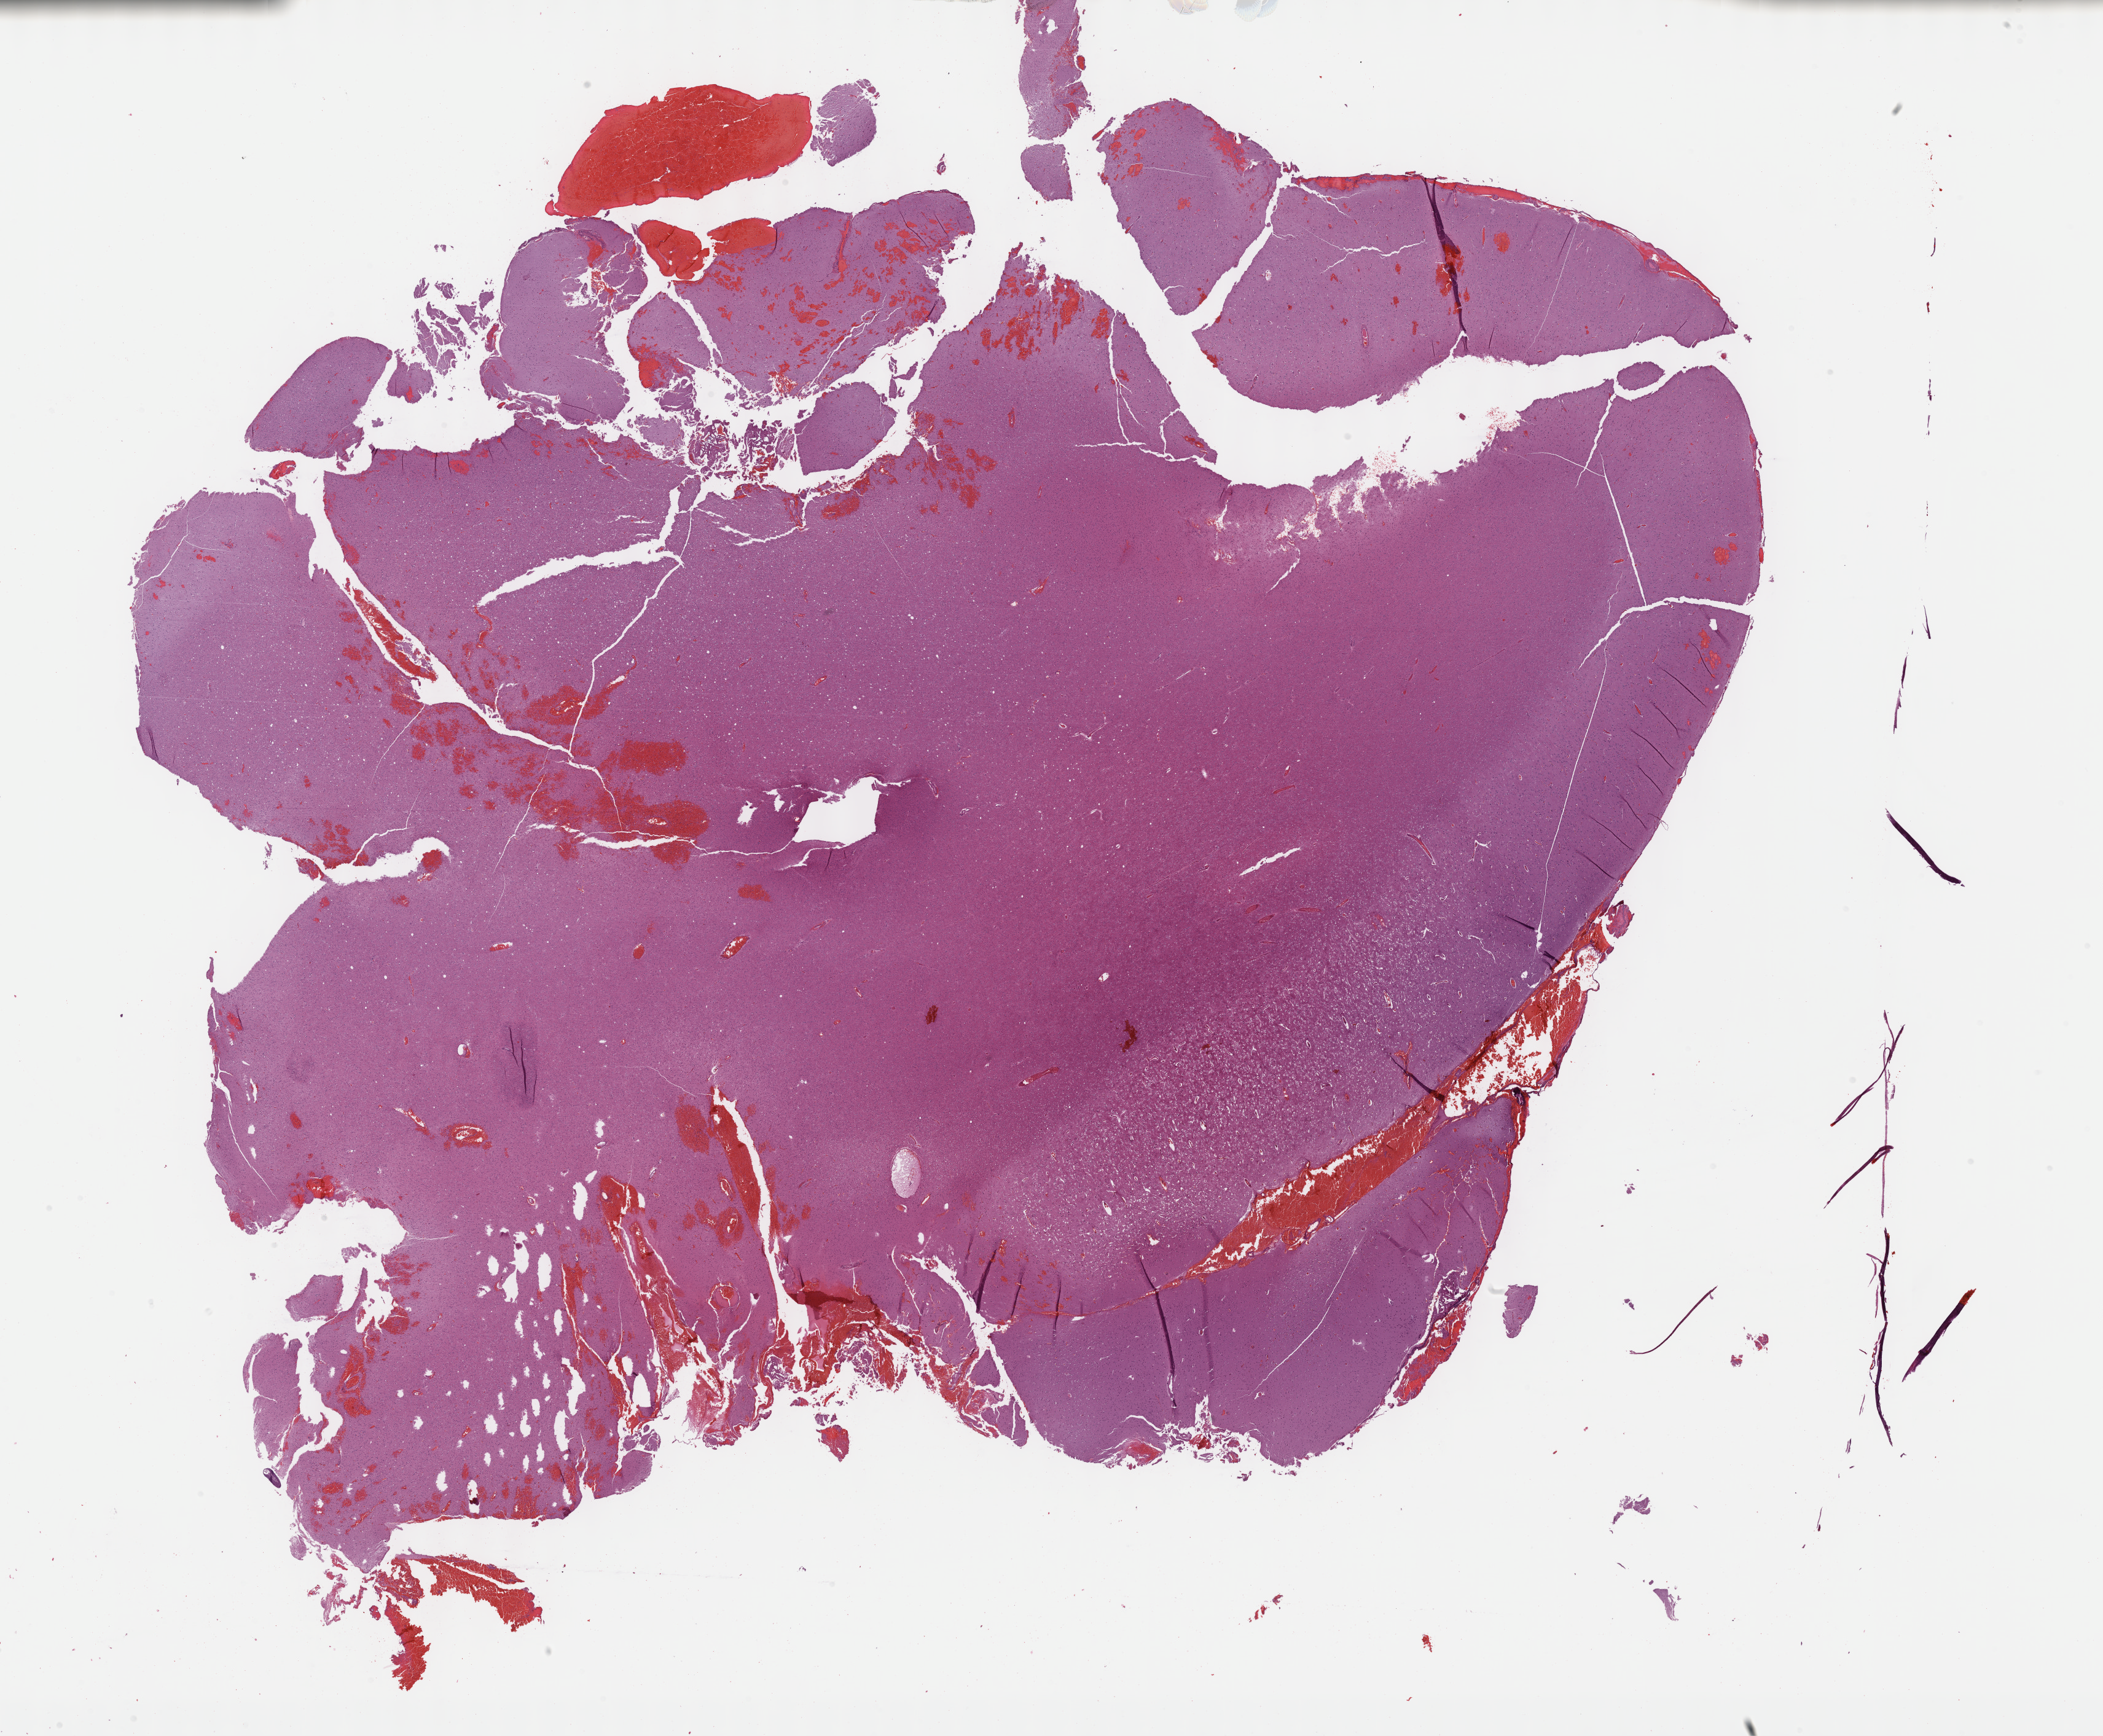
Hematoxylin and eosin (H&E) stained whole-slide image — whole scanned area (about 27.7 x 22.9 mm, acquisition: 40x scan) shown as a low-resolution overview; formalin-fixed paraffin-embedded (FFPE) diagnostic section; brain, primary tumour sample. Male patient; age at initial diagnosis 61 years. Histologic grade: G2 (moderately differentiated).
Laterality: right. Pathologic diagnosis: Mixed glioma (cerebrum).